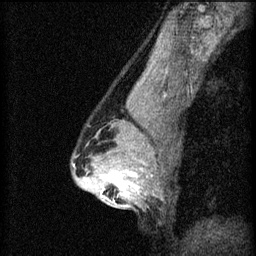
Breast MRI (dynamic contrast-enhanced), one sagittal slice. Slice 41 of 60 in the series (ordered by position). 3 images stored at this slice position (order not interpretable as contrast timing). 1.5 T. TE 4.2 ms, TR 8.2 ms. 2 mm slice thickness. 256 × 256 image matrix. Female patient, age 44 years.
Structures marked on this image (semi-automatic segmentation, software-assisted and operator-edited):
- analysis volume of interest (the breast-tissue region the enhancement analysis was run in; not a lesion): bounding box [x1, y1, x2, y2] px = [94, 162, 143, 205]
- tumour enhancement mask (voxels above the 70 % enhancement threshold inside the analysis volume of interest): [100, 168, 143, 201]